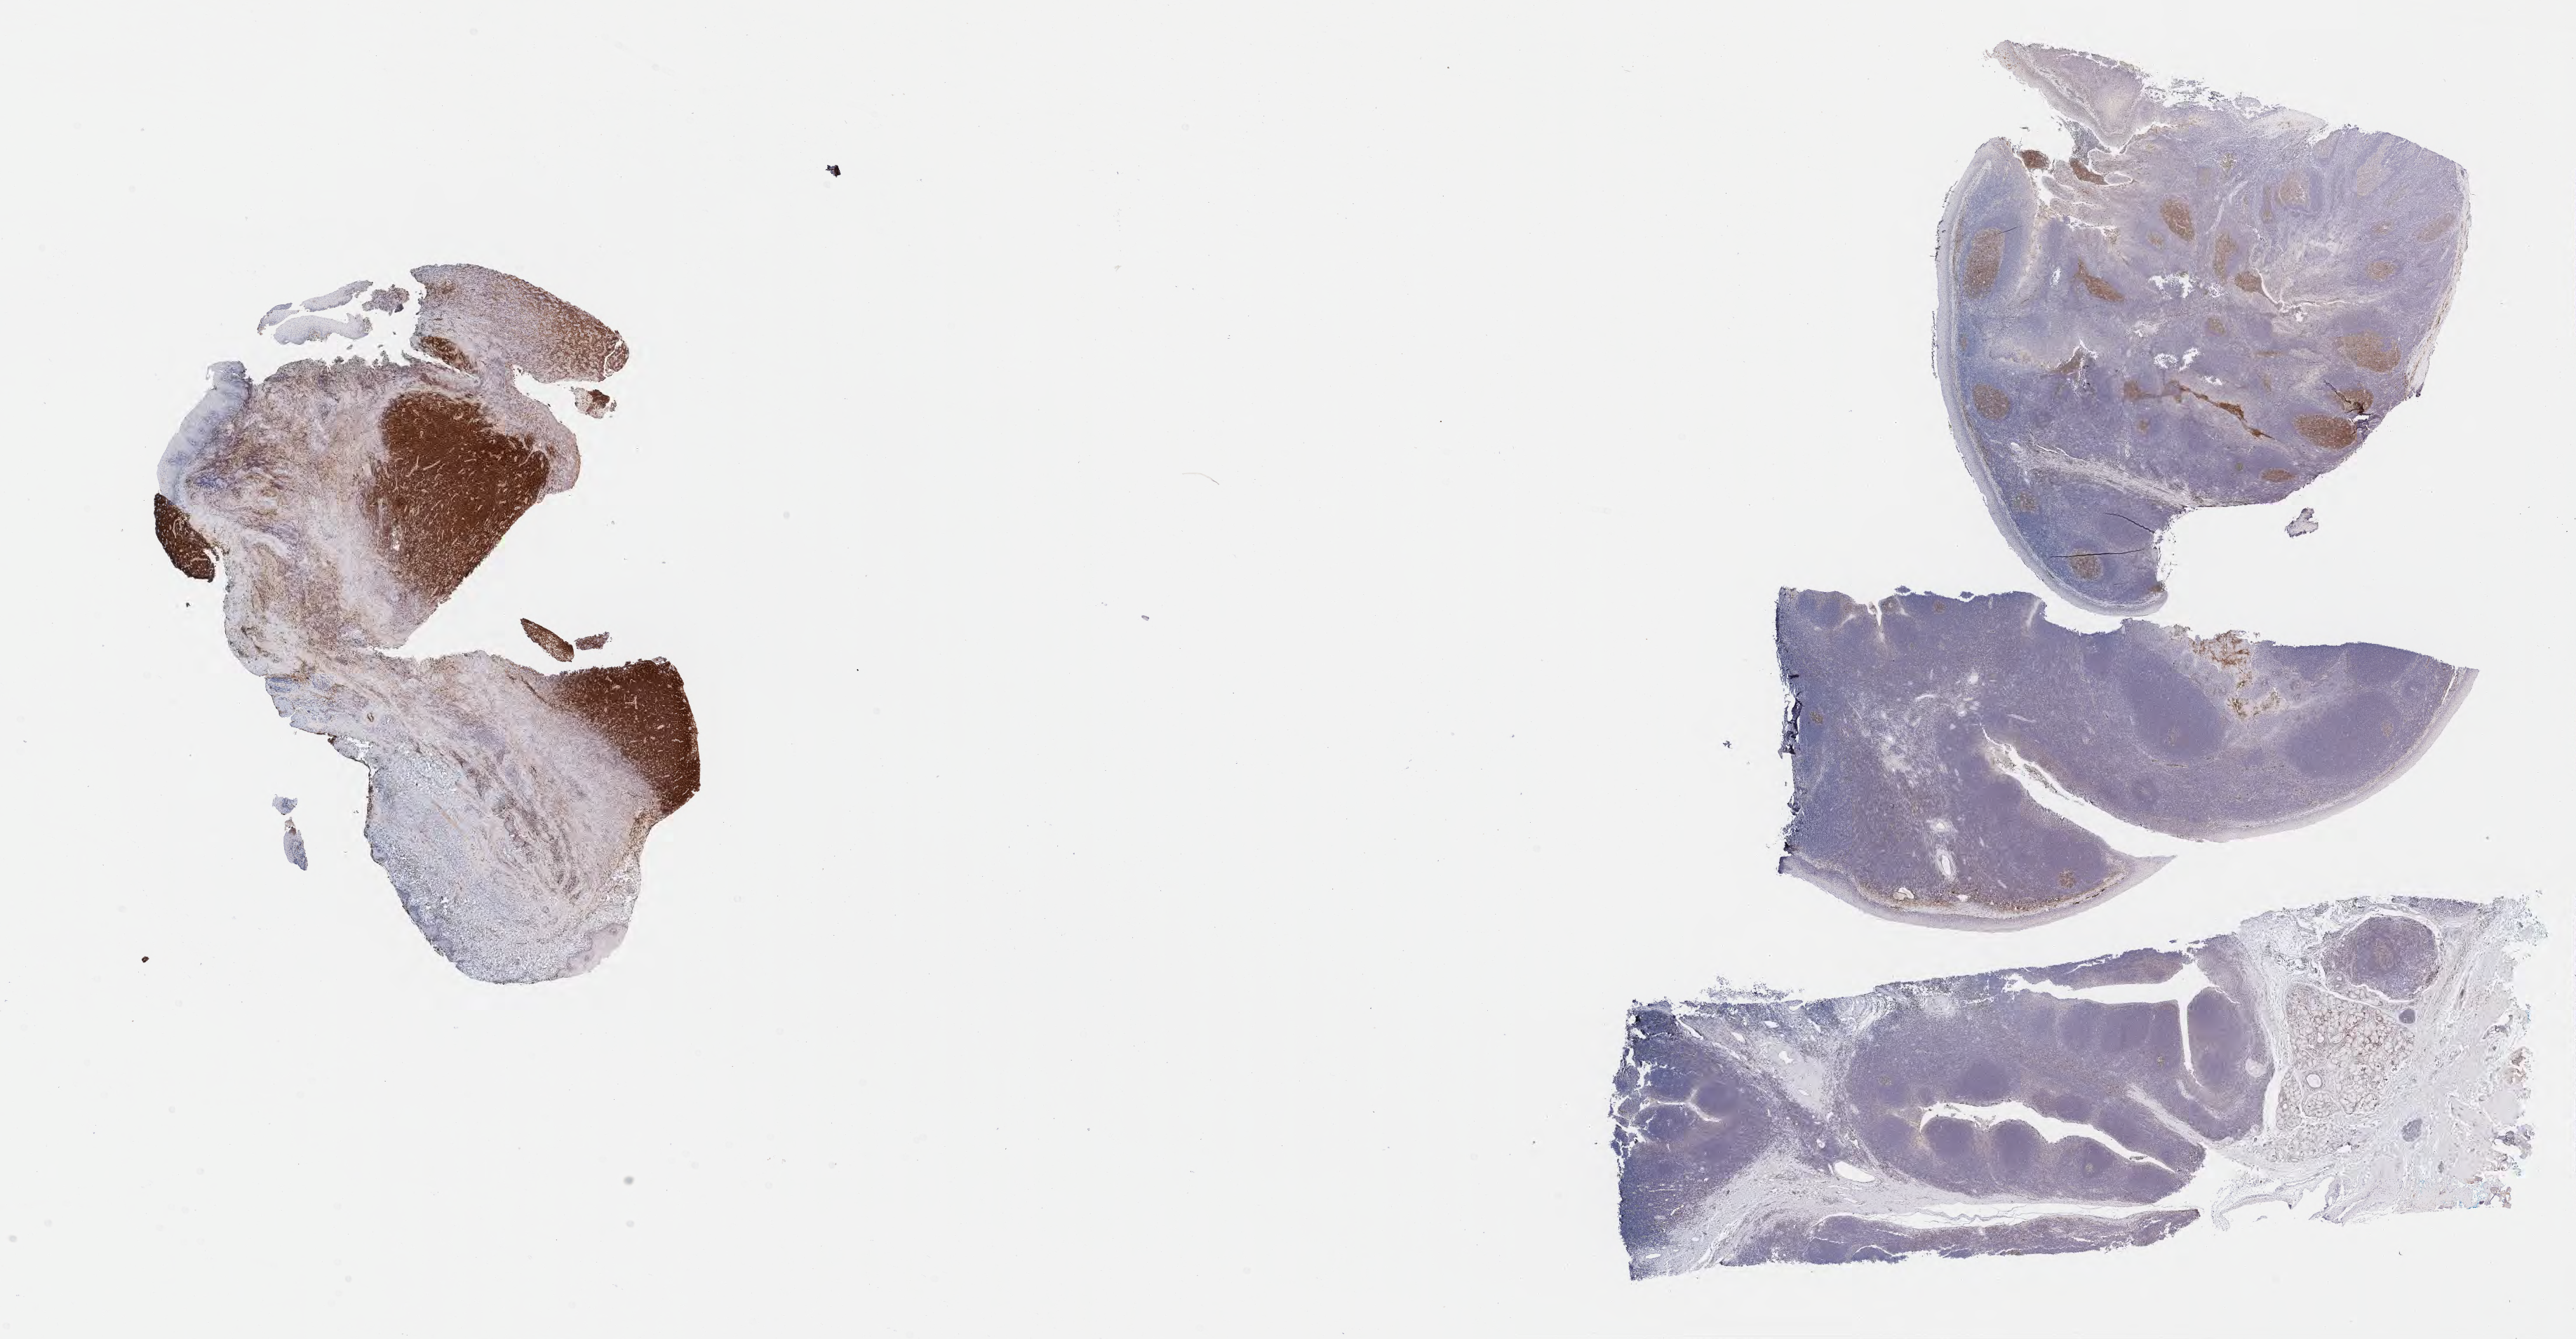
IHC for CD10, whole-slide image, low-resolution overview of the scanned area, about 29.7 x 15.4 mm. Specimen: tumor tissue. Site: cranium. Patient: male, age 10 years.
* diagnosis: Burkitt lymphoma, NOS